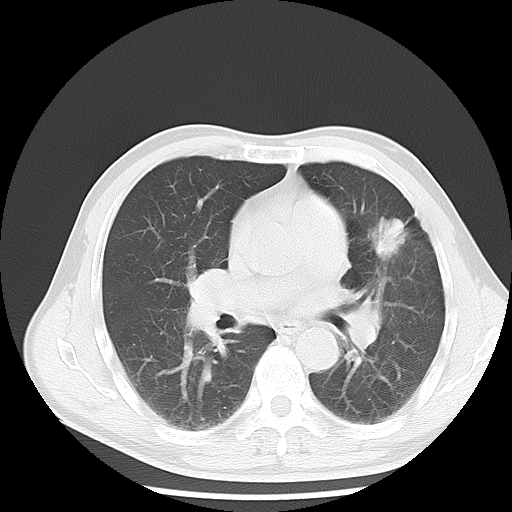
Chest CT, one axial slice. Slice 5 of 9 in the series (ordered by position). Lung window (W 1500 / L -600 HU). 512 × 512 image matrix, field of view 350 × 350 mm. Male patient, age 54 years. Case-level facts recorded for this patient, not image findings: clinical TNM (as recorded): T1c N0 M0.
Outlined on this slice (rectangle marked by the reading radiologist):
- lung tumour (recorded histology: adenocarcinoma): bounding box (x1, y1, x2, y2) in pixels: (369, 211, 413, 262)